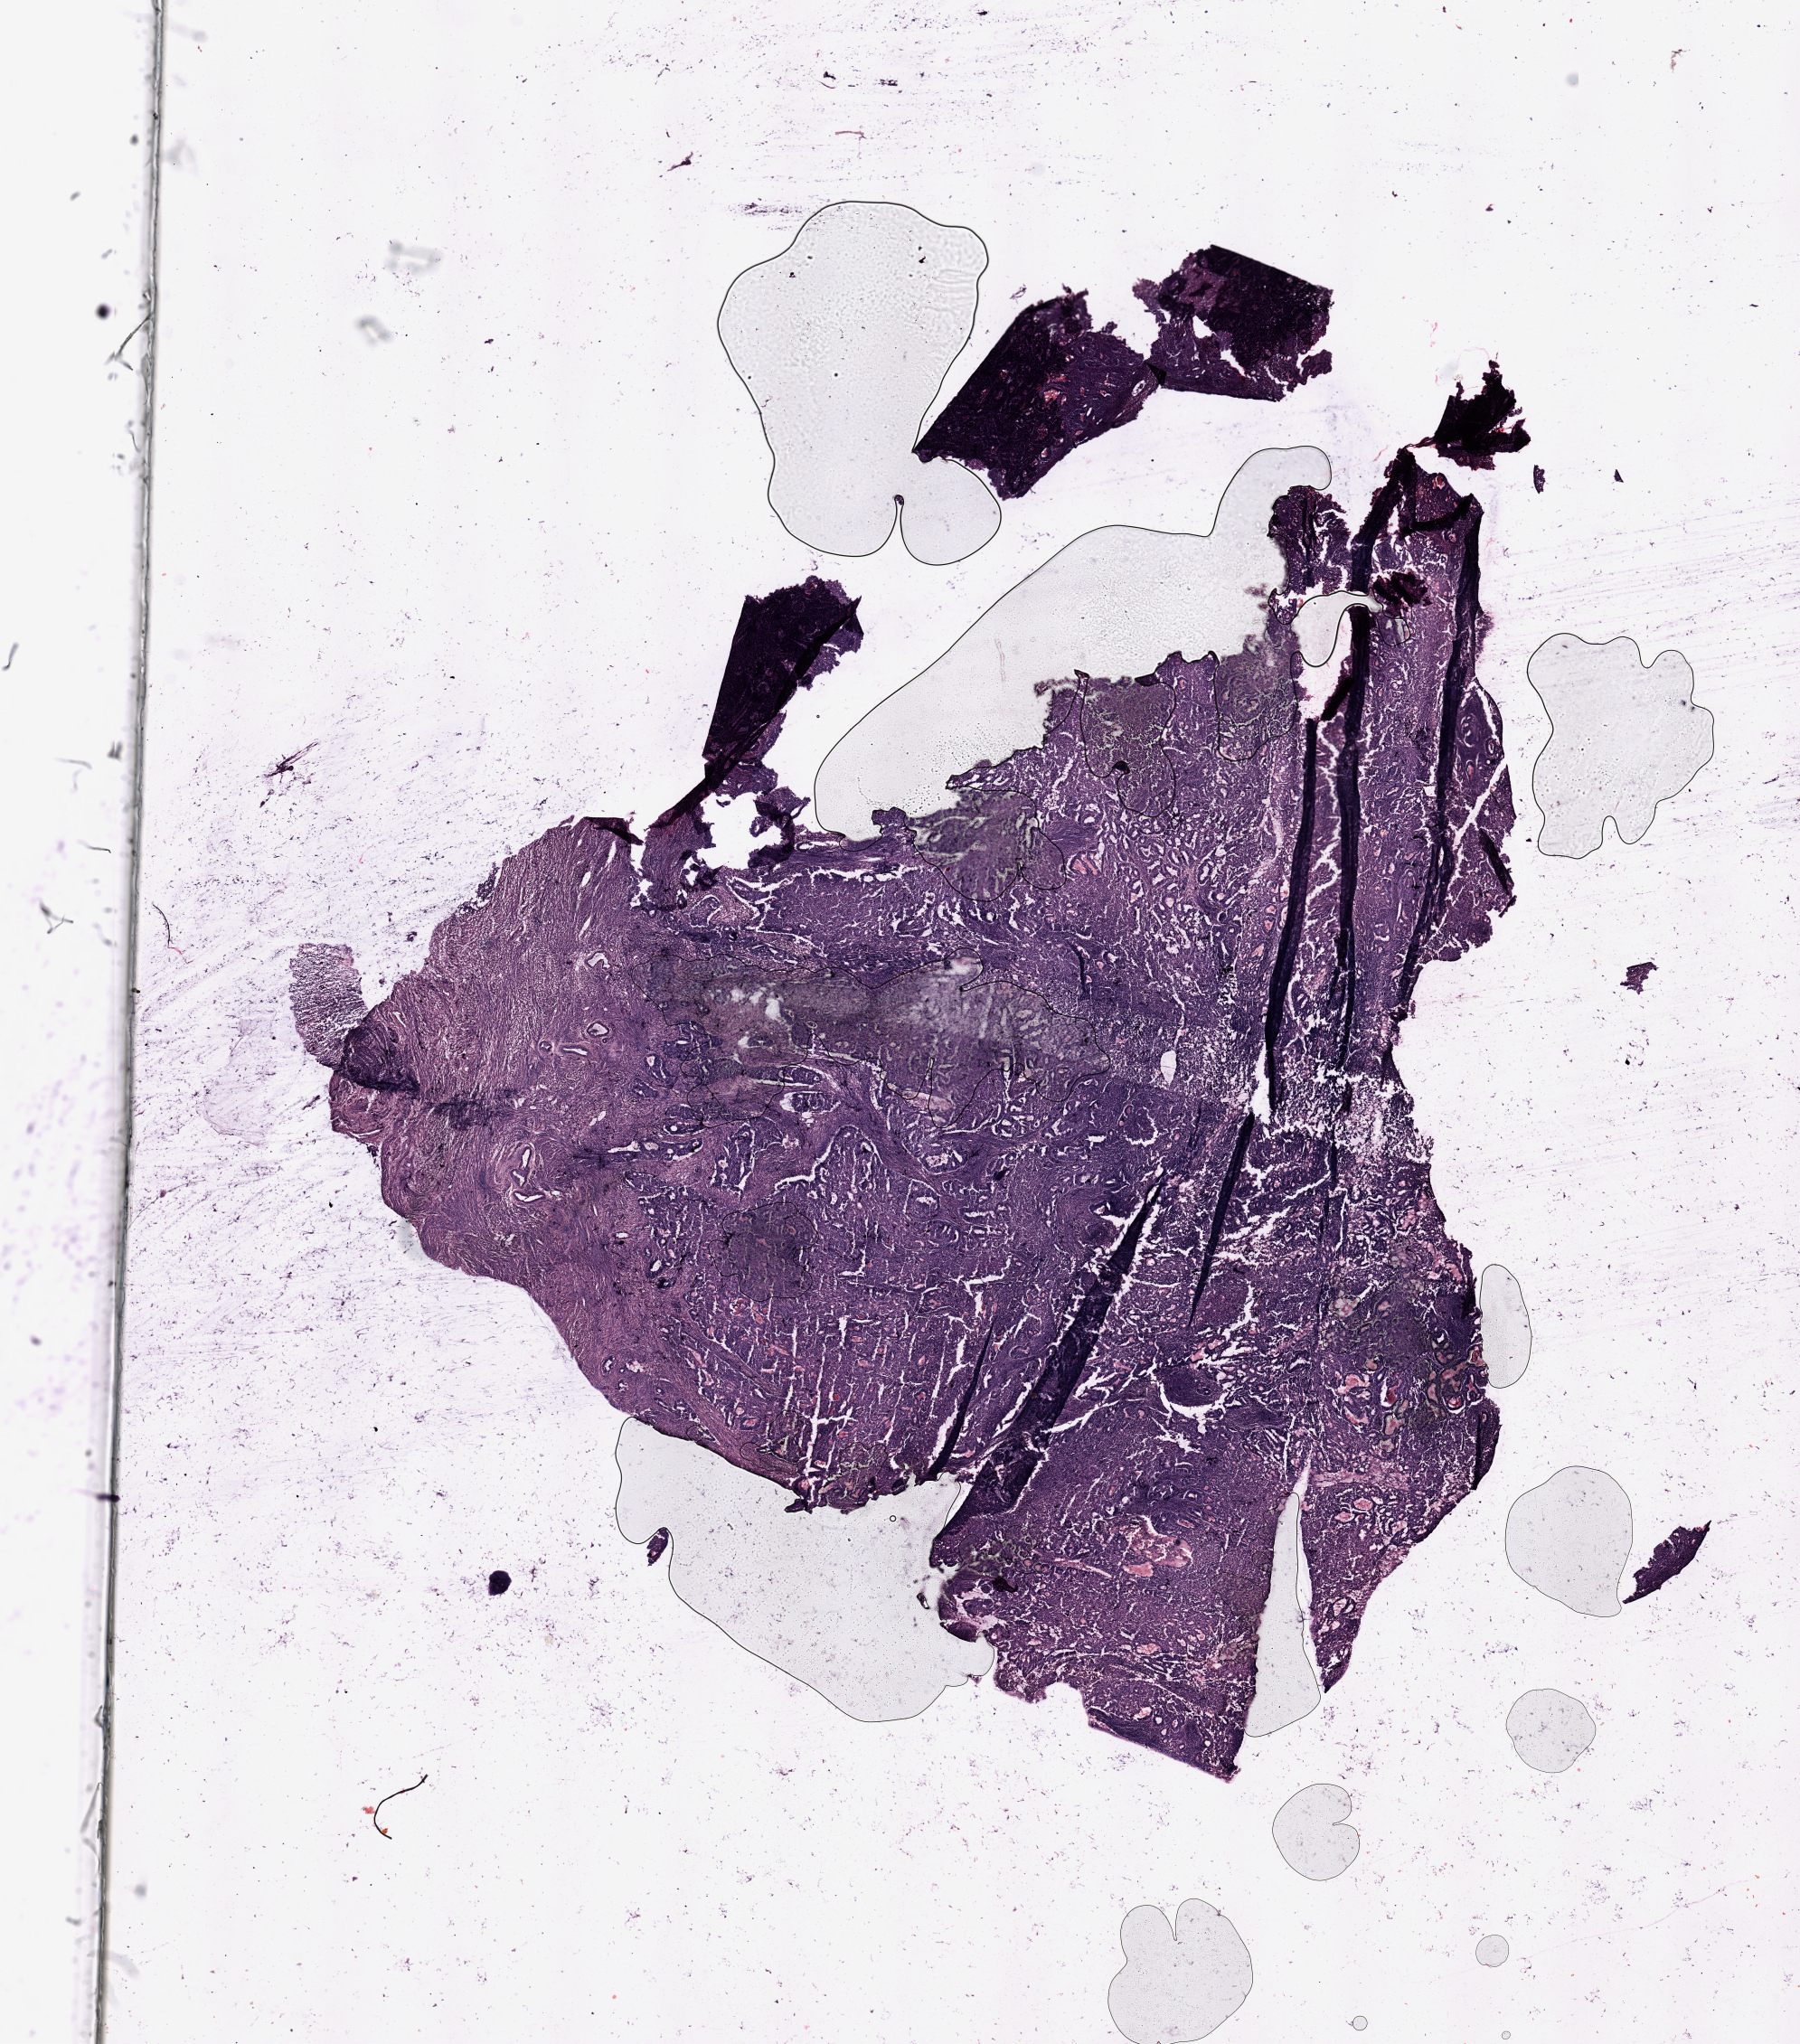
Whole-slide histology image, H&E-stained, shown as a low-resolution overview of the whole scanned area (about 15.8 x 17.9 mm). Tumour tissue sample, sampled site: uterus. Patient: female, age 62 years. Histologic grade: G2 (moderately differentiated). Composition of this section per pathologist review: tumour nuclei 80%, necrosis 0%.
* AJCC pathologic stage: I
* diagnosis: Endometrioid adenocarcinoma, NOS